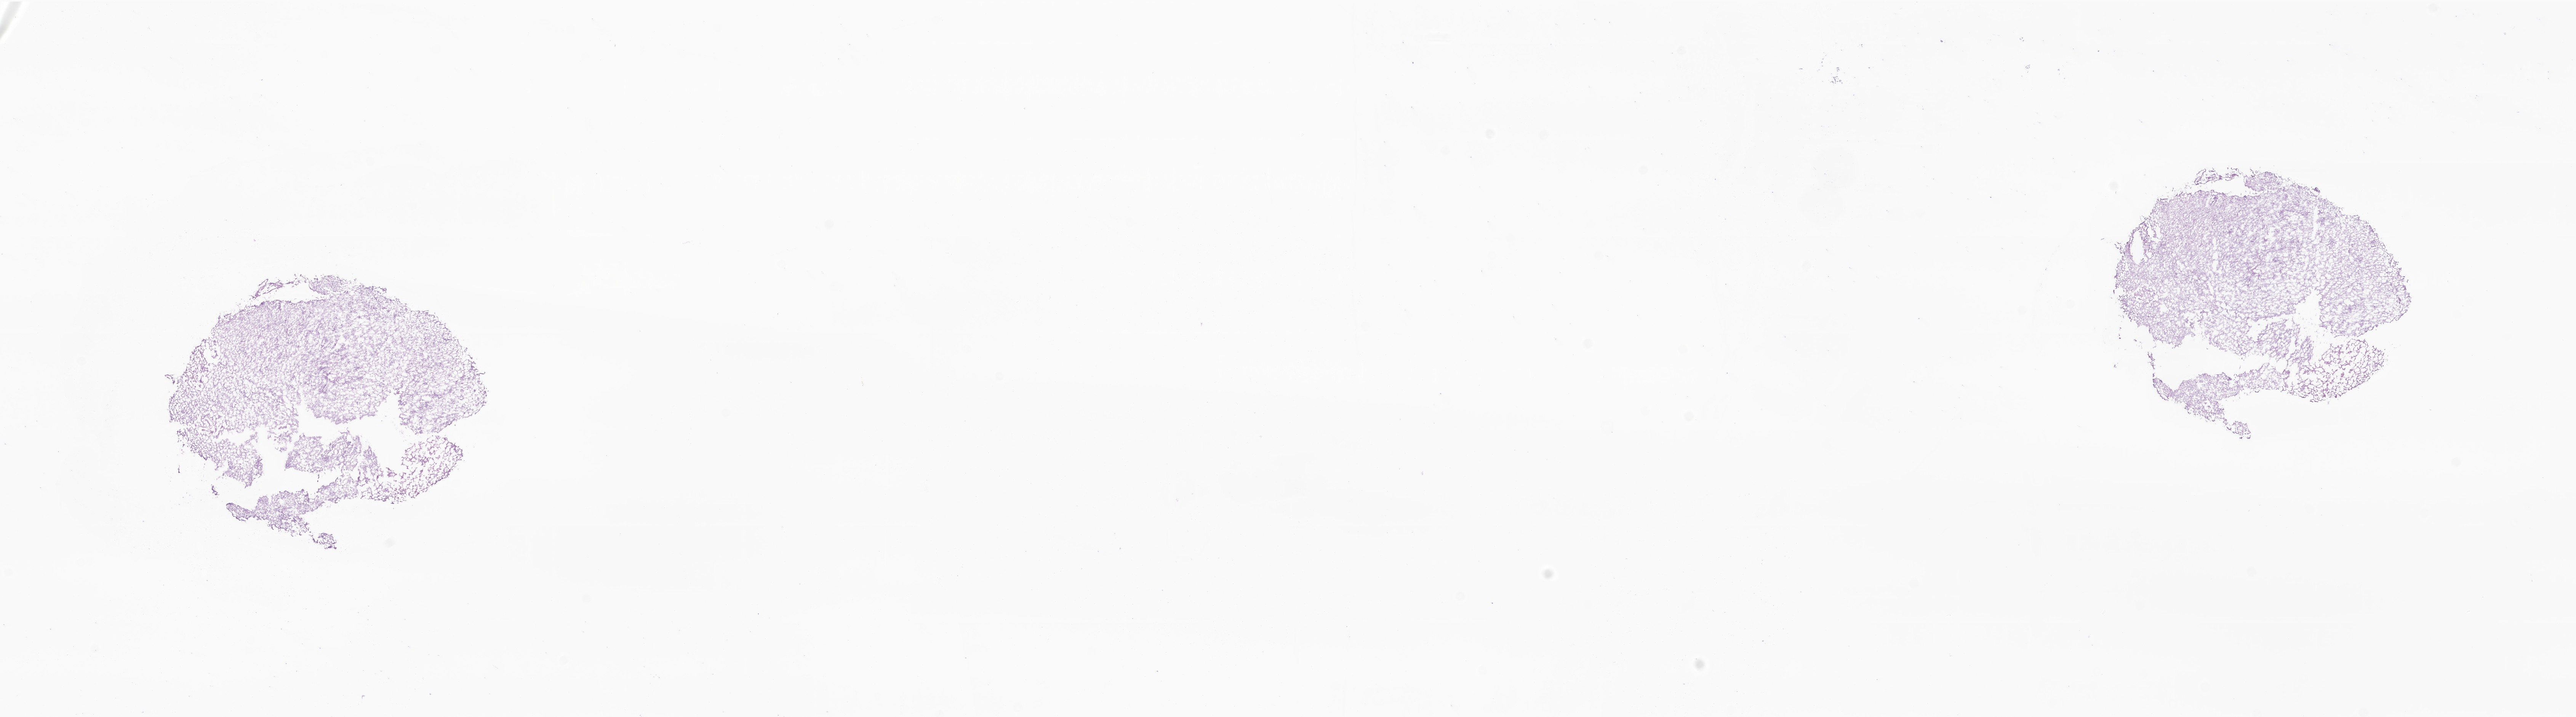
Digitized hematoxylin and eosin (H&E)-stained section of tumor tissue from the brain, shown as a low-resolution overview of the whole scanned area (about 28.5 x 7.9 mm); cryosection (OCT / tissue freezing medium). Female patient, age 37 months (3 years 1 month).
Recorded diagnosis: Glioma, malignant.